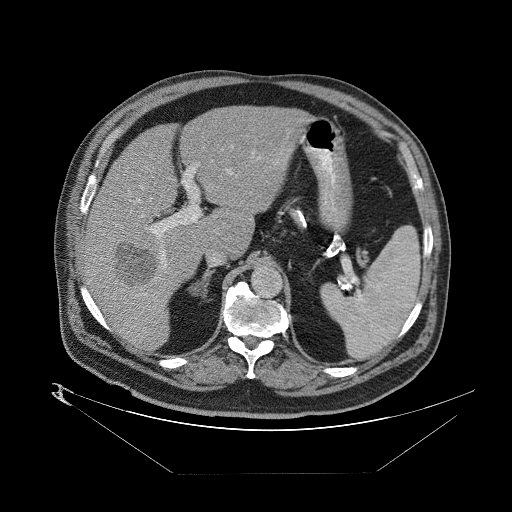
Contrast-enhanced abdominal CT (liver protocol), one axial slice; slice 51 of 89 in the series (ordered by position); reconstruction kernel STANDARD; 140 kVp; one of 2 acquisitions stored at this slice position; soft-tissue window (W 400 / L 40 HU); 2.5 mm slice thickness; 512 × 512 image matrix. From the clinical record (not read from this slice): diagnosis: hepatocellular carcinoma (patient treated with transarterial chemoembolisation; whether this scan precedes or follows treatment is not stated here); TNM stage (as recorded): Stage-II; Child-Pugh class: B; tumour differentiation: moderately differentiated; tumour size: 4 cm.
Outlined on this slice (semi-automatic segmentation, software-assisted and operator-edited):
- abdominal aorta: bounding box <253,267,282,296> (left, top, right, bottom; pixels)
- liver parenchyma outside the tumour (the mass and vessels are separate outlines, so this box may not span the whole liver): <80,102,304,348>
- mass: <110,237,158,289>
- liver vessels: <87,144,259,326>